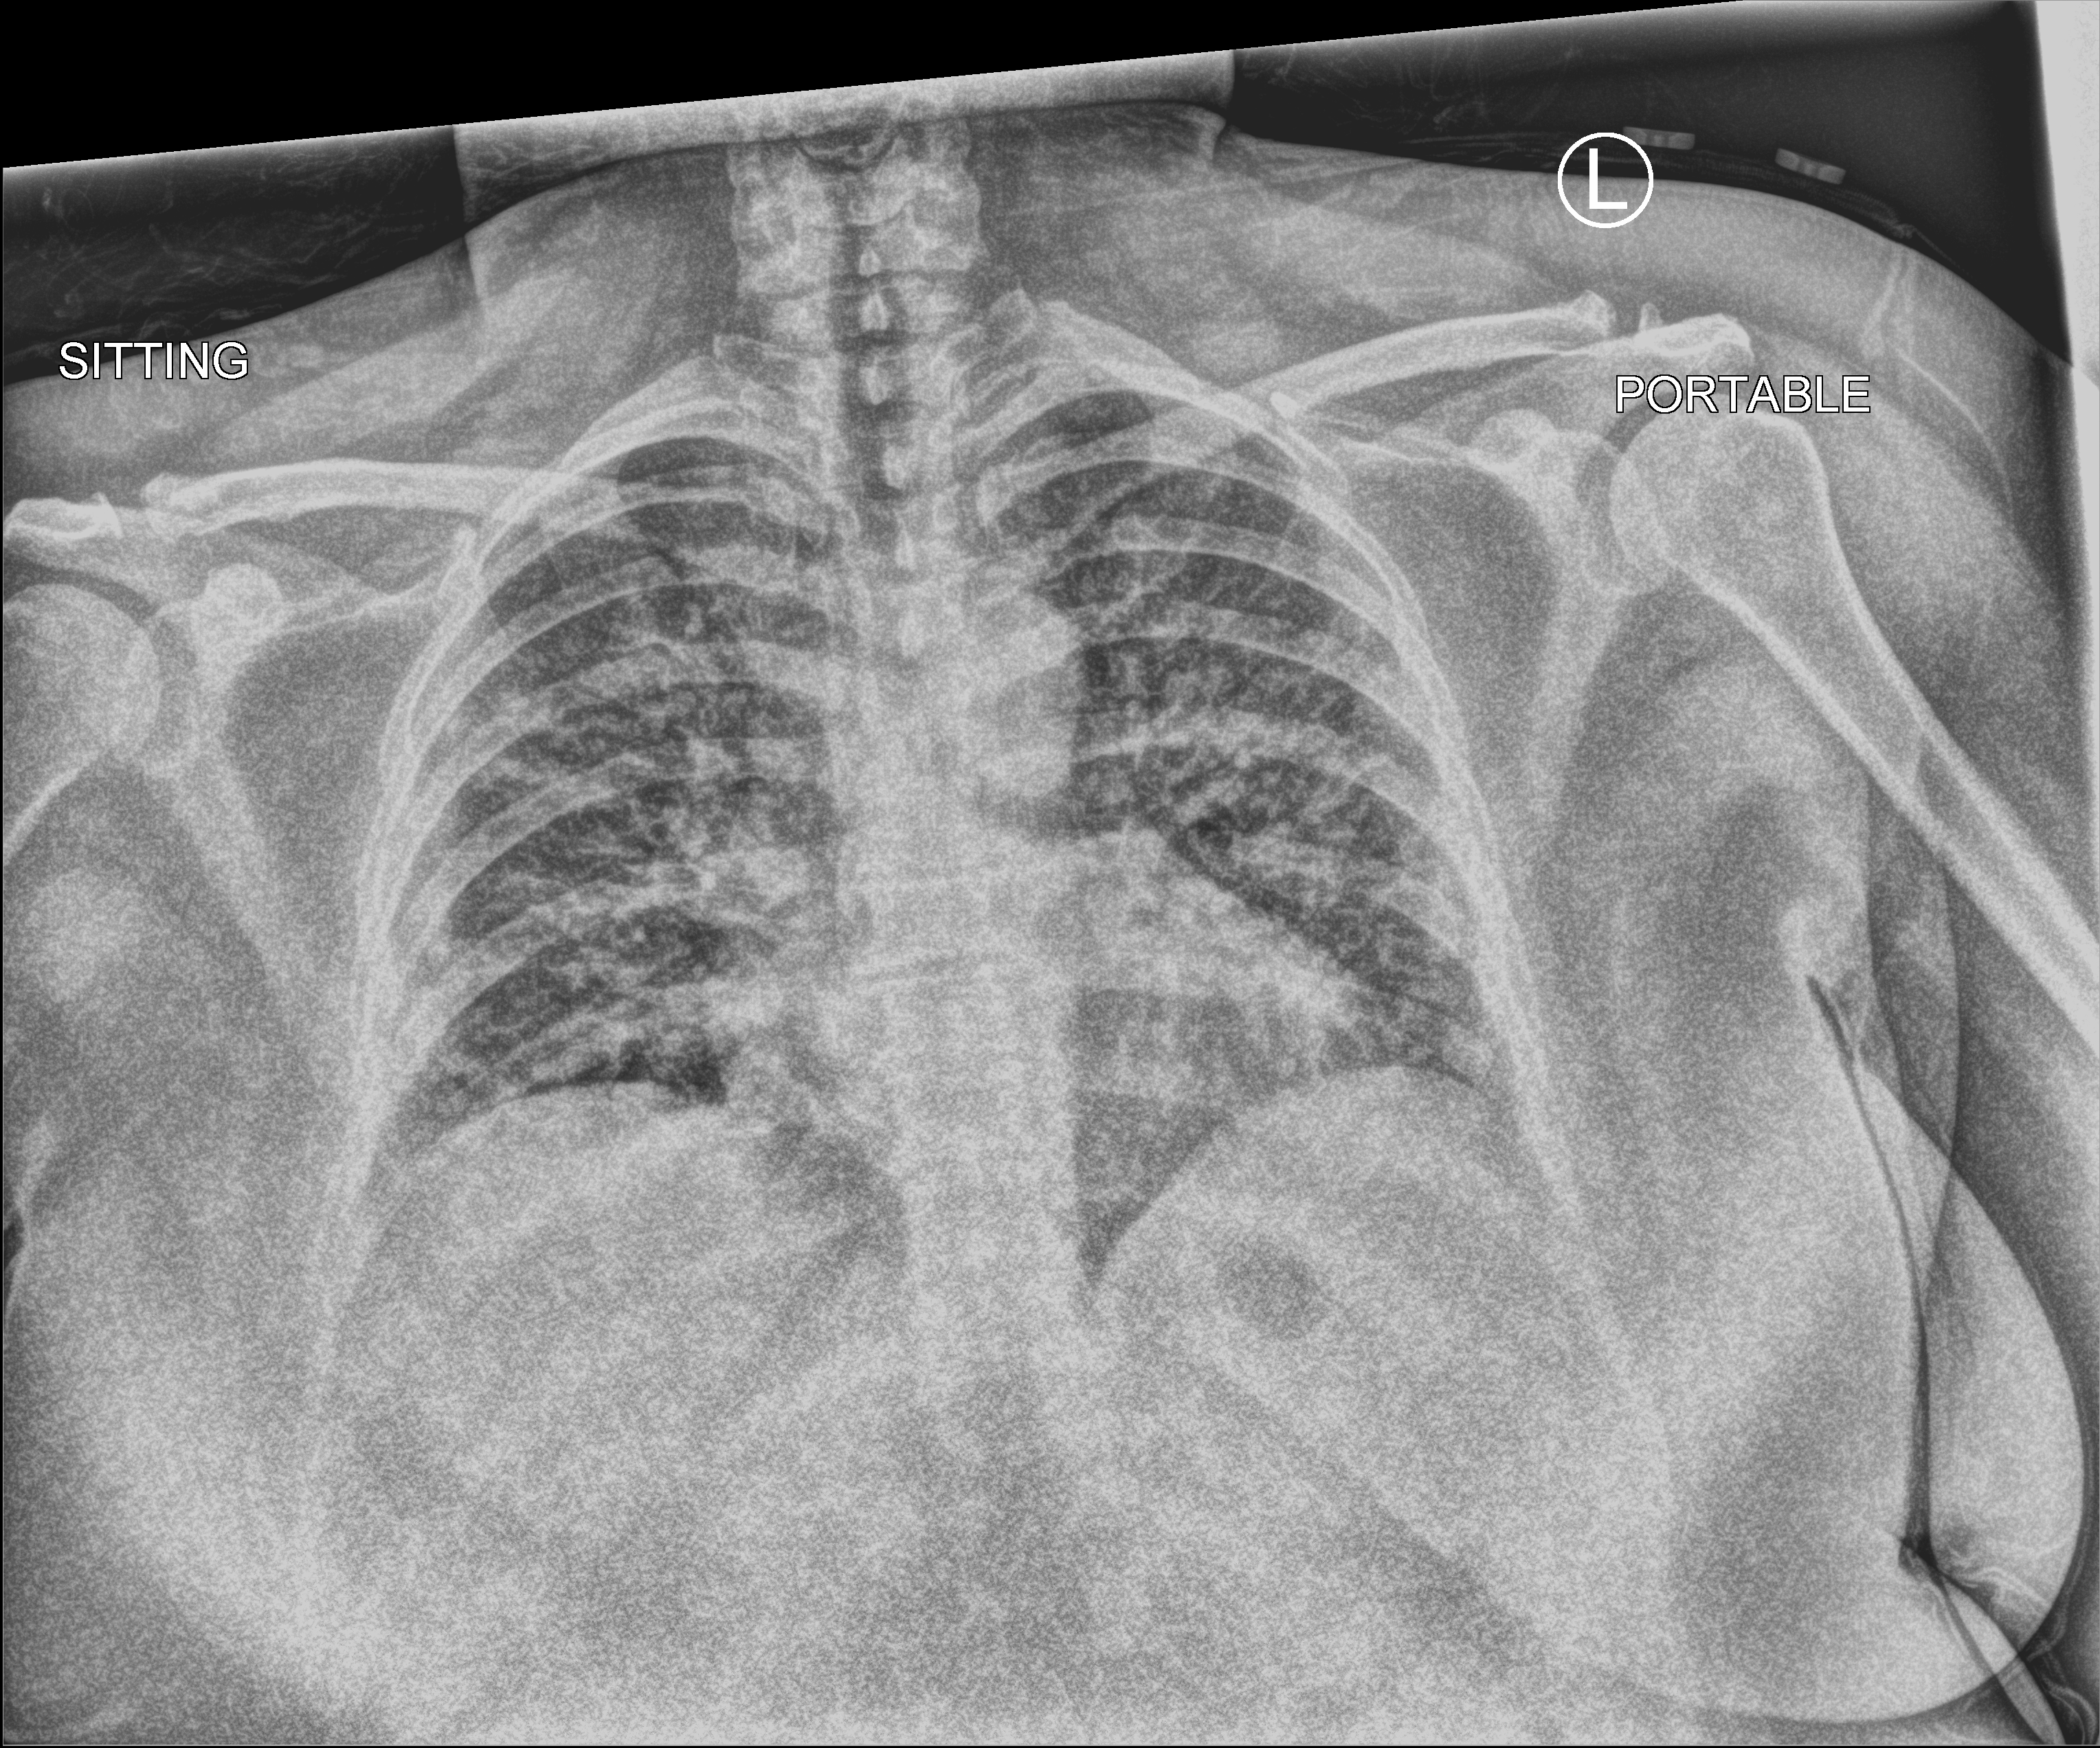
Portable chest radiograph, anteroposterior (AP) projection. Patient hospitalised with COVID-19; female, aged 18–59 years.
From the hospital-stay record, not from the radiograph (when in the stay this image was taken is not recorded): smoking status (admission record): never; length of hospital stay: 95 days.